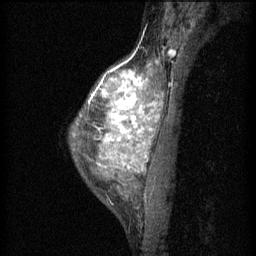
Breast MRI (dynamic contrast-enhanced), one sagittal slice. Position 41 of 60 along the scan axis. 3 images stored at this slice position (order not interpretable as contrast timing). 1.5 T. TE 4.2 ms, TR 11 ms. 256 × 256 image matrix, field of view 180 × 180 mm. Patient: female, 40 years.
Annotated regions visible in this slice (semi-automatic segmentation, software-assisted and operator-edited):
- analysis volume of interest (the breast-tissue region the enhancement analysis was run in; not a lesion): box from (x=71, y=48) to (x=166, y=203) px
- tumour enhancement mask (voxels above the 70 % enhancement threshold inside the analysis volume of interest): (x=89, y=66)–(x=162, y=171)